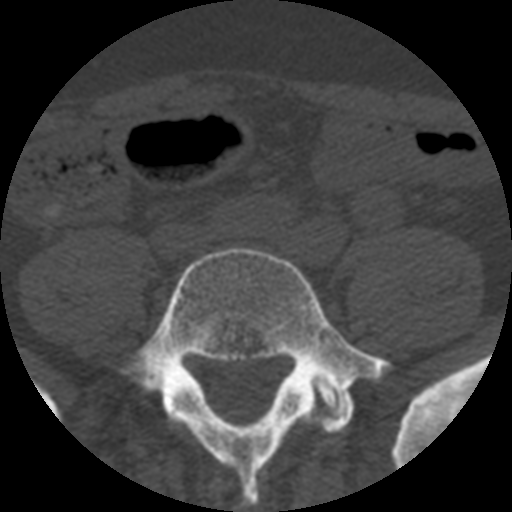
CT including the spine, one axial slice; slice 64 of 508 in the series (ordered by position); reconstruction kernel STANDARD; 120 kVp; bone window (W 1800 / L 400 HU); 1.25 mm slice thickness; 512 × 512 image matrix. Patient age 57 years. From the clinical record (not read from this slice): primary cancer: prostate.
Structures marked on this image (semi-automatic segmentation, software-assisted and operator-edited):
- L5 vertebra: bounding box <120,247,391,512> (left, top, right, bottom; pixels)